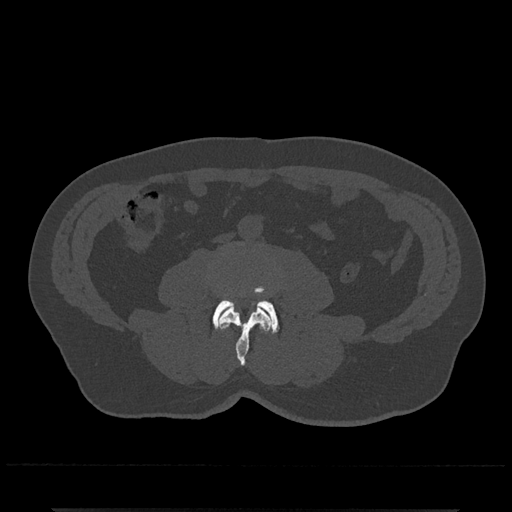
CT including the spine, one axial slice; slice 191 of 797 in the series (ordered by position); reconstruction kernel Br40s/3; 120 kVp; bone window (W 1800 / L 400 HU); 0.5 mm slice thickness; 512 × 512 image matrix, field of view 393 × 393 mm. Male patient, age 67 years. From the clinical record (not read from this slice): primary cancer: prostate.
Structures marked on this image (semi-automatically segmented with operator editing):
- L3 vertebra: bounding box (x1, y1, x2, y2) in pixels: (218, 306, 272, 365)
- L4 vertebra: (212, 287, 280, 333)